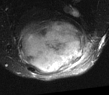
MRI of an extremity soft-tissue mass, one axial slice. Slice 26 of 52 in the series (ordered by position). T2-weighted fat-saturated. MR volume resampled by the dataset authors to the PET/CT grid (not the native acquisition matrix). 109 × 95 image matrix, field of view 106 × 93 mm. Male patient. Case-level facts recorded for this patient, not image findings: histological type: synovial sarcoma; site of the primary tumour: left poplietal fossa.
Structures marked on this image (expert contour drawn on MRI and transferred to this co-registered scan by the dataset authors):
- gross tumour volume (mass): bounding box [x1, y1, x2, y2] px = [15, 17, 86, 75]